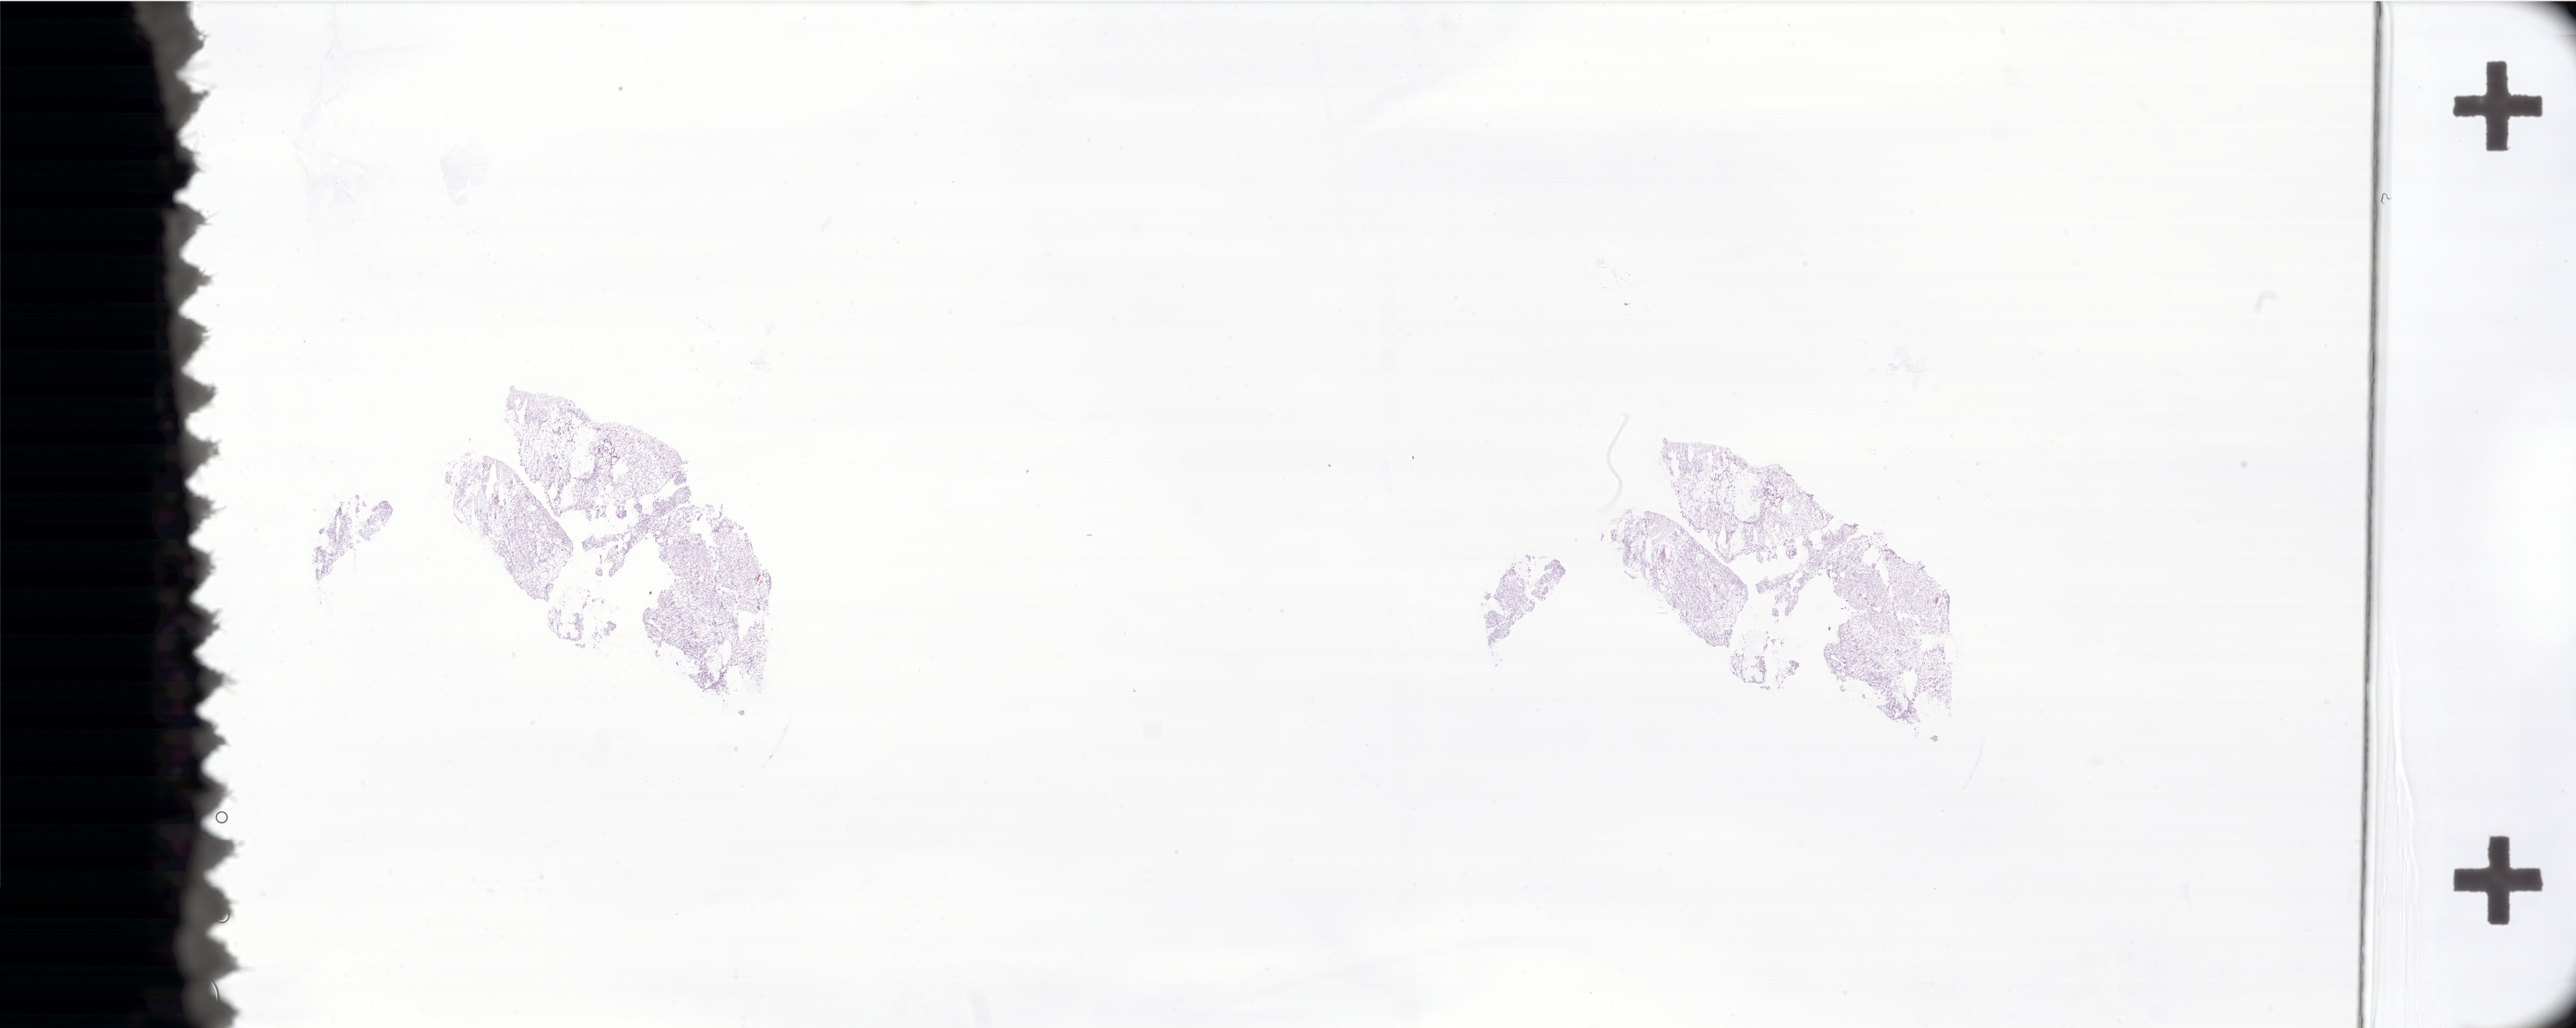
Whole-slide image, H&E stain of tumor tissue from the brain, shown as a low-resolution overview of the whole scanned area (about 58.1 x 23.2 mm), frozen section (OCT-embedded). Patient: male, age 82 months (6 years 10 months).
Recorded diagnosis: Pilocytic astrocytoma.